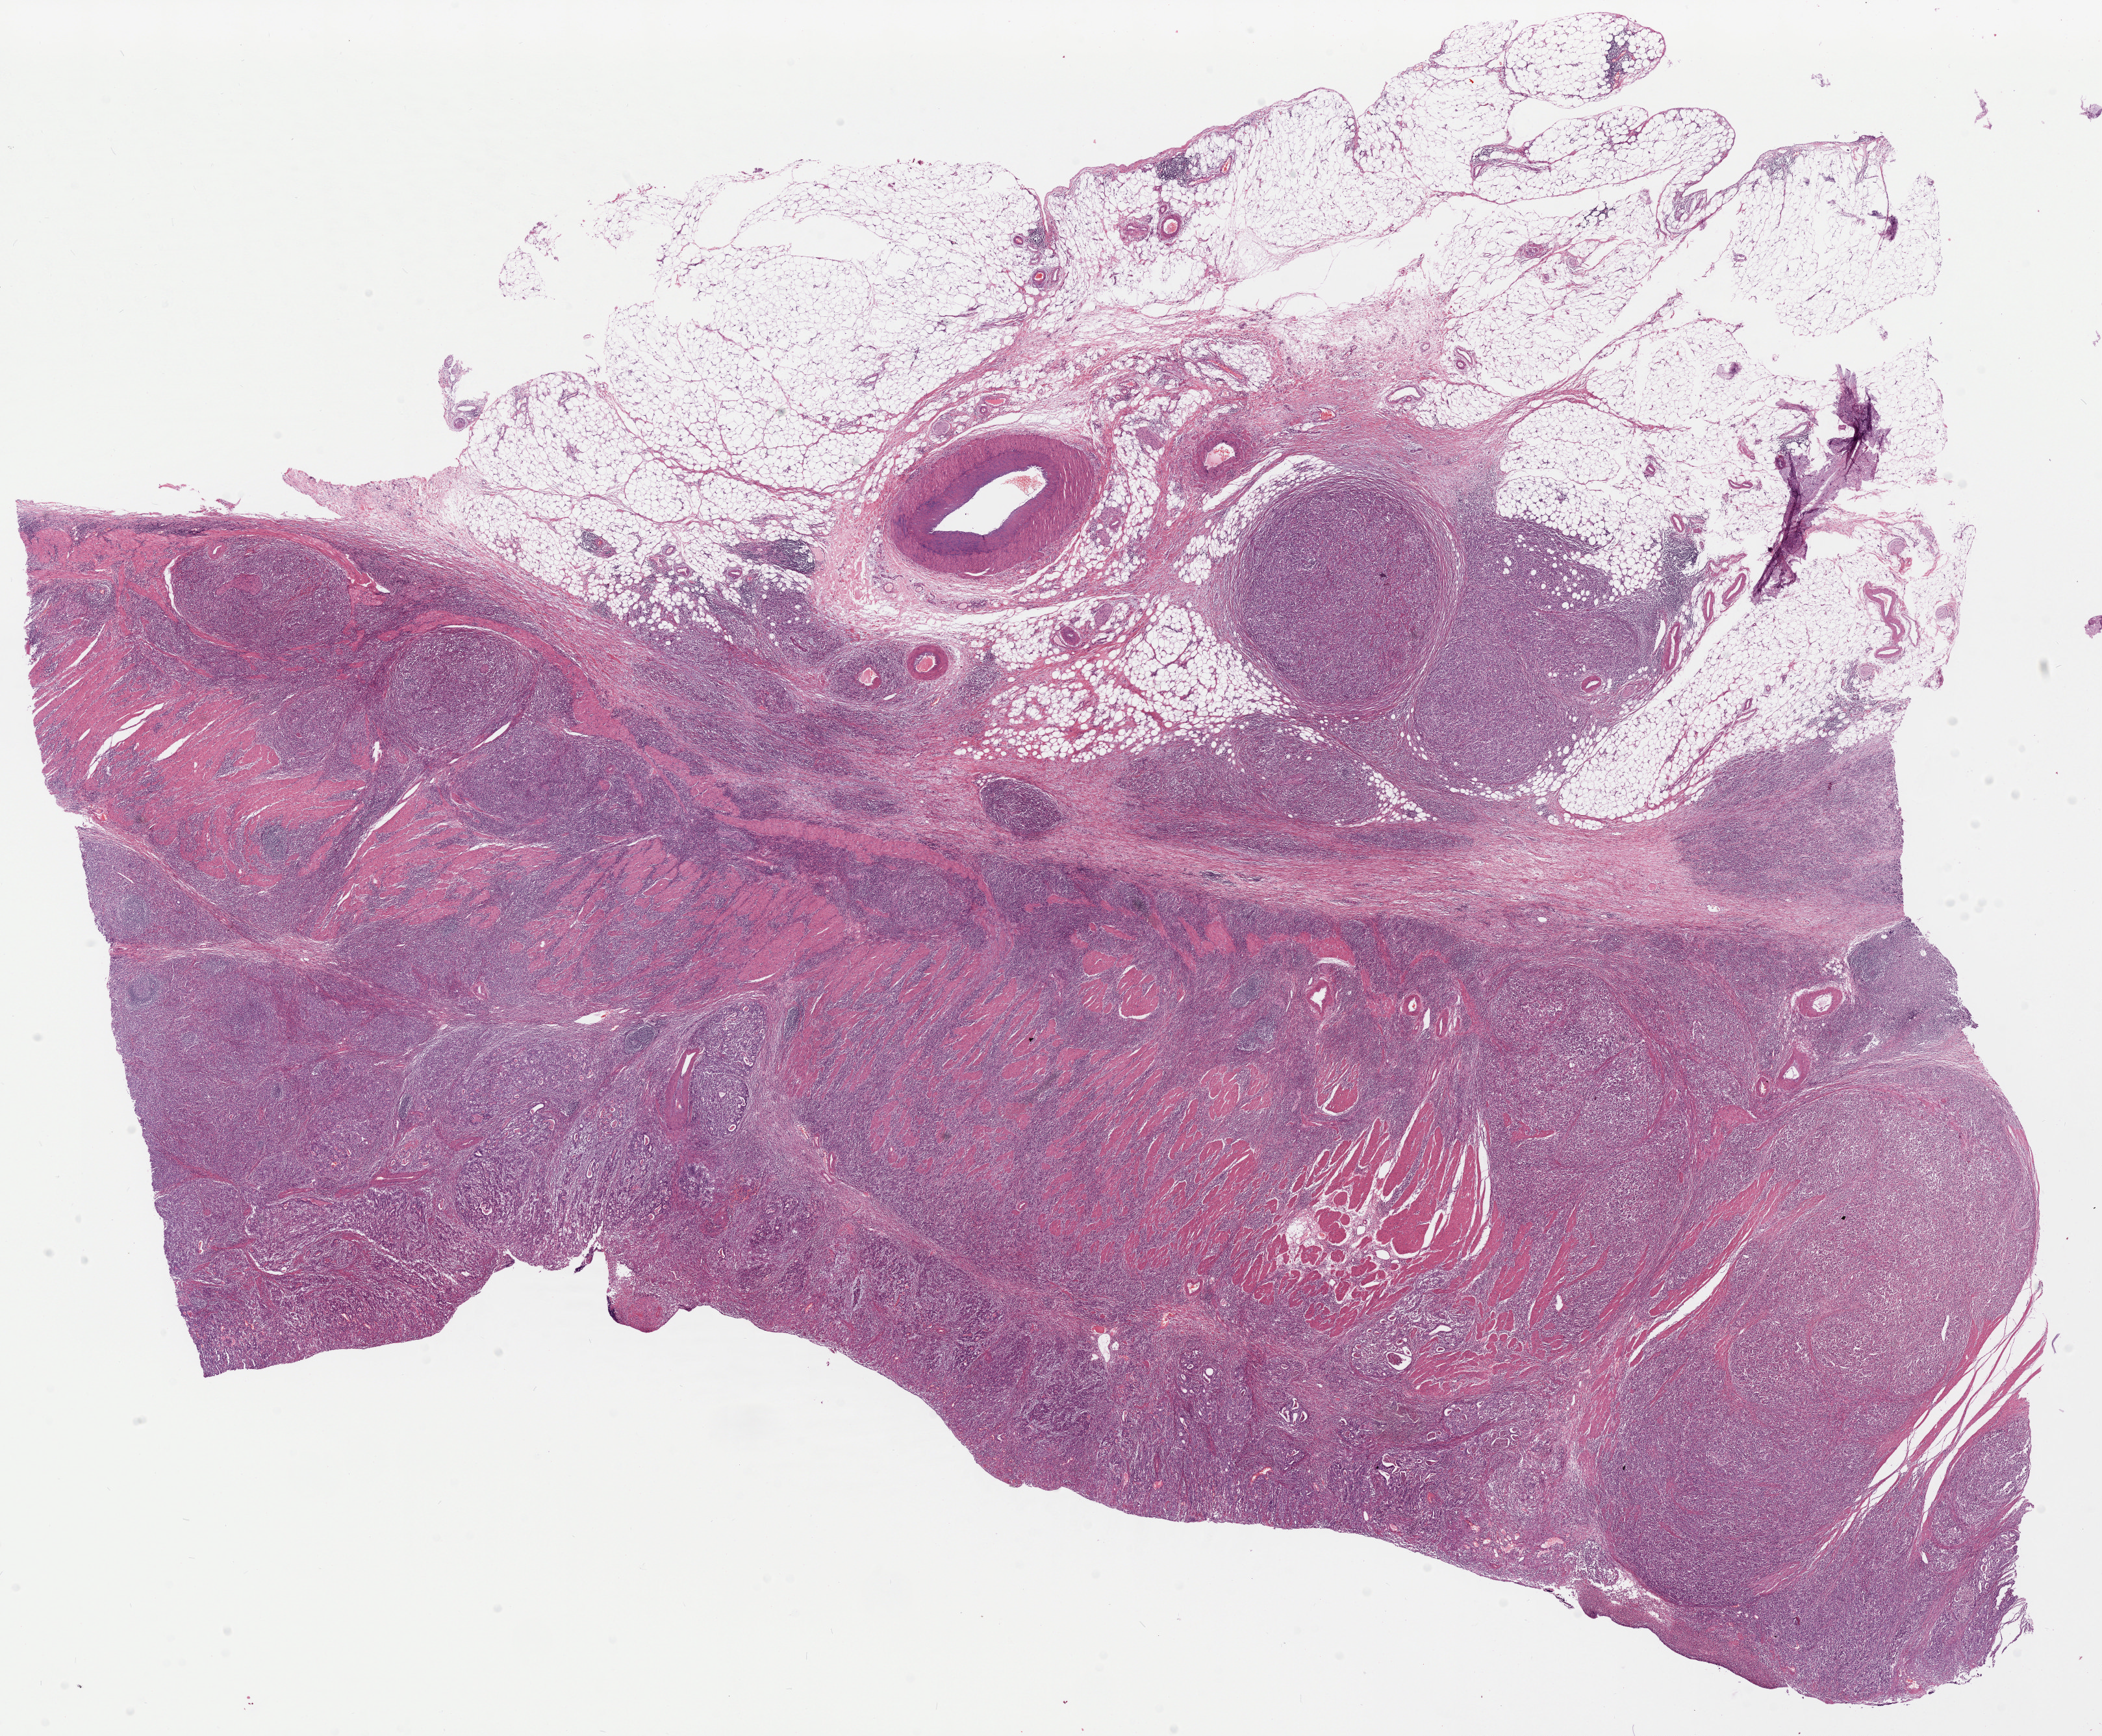
Digitized H&E-stained tissue section (whole slide), a low-resolution overview of the entire scanned area, about 25.6 x 21.1 mm (from a 20x scan). Formalin-fixed paraffin-embedded (FFPE) diagnostic section. Primary tumour sample from the stomach. Patient: male, age at initial diagnosis 70 years. Histologic grade: G3 (poorly differentiated).
- AJCC pathologic stage: IIIB
- diagnosis: Carcinoma, diffuse type (body of stomach)